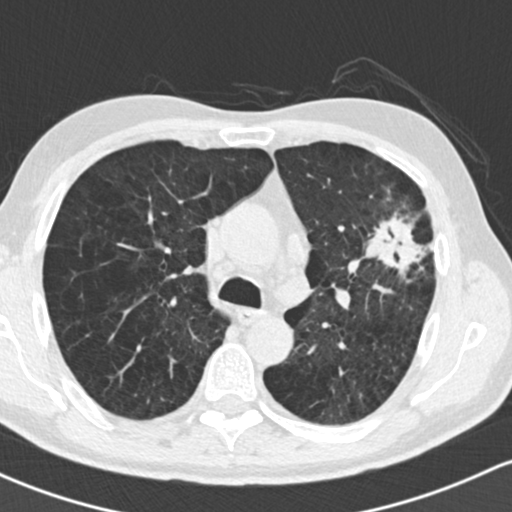
Low-dose screening chest CT, one axial slice; position 104 of 162 along the scan axis; 120 kVp; lung window (W 1500 / L -600 HU); 2 mm slice thickness; 512 × 512 image matrix.
Annotated regions visible in this slice (outlined manually by an expert reader):
- lesion 1 (tumor, upper lobe of left lung): bounding box (x1, y1, x2, y2) in pixels: (366, 212, 434, 274)